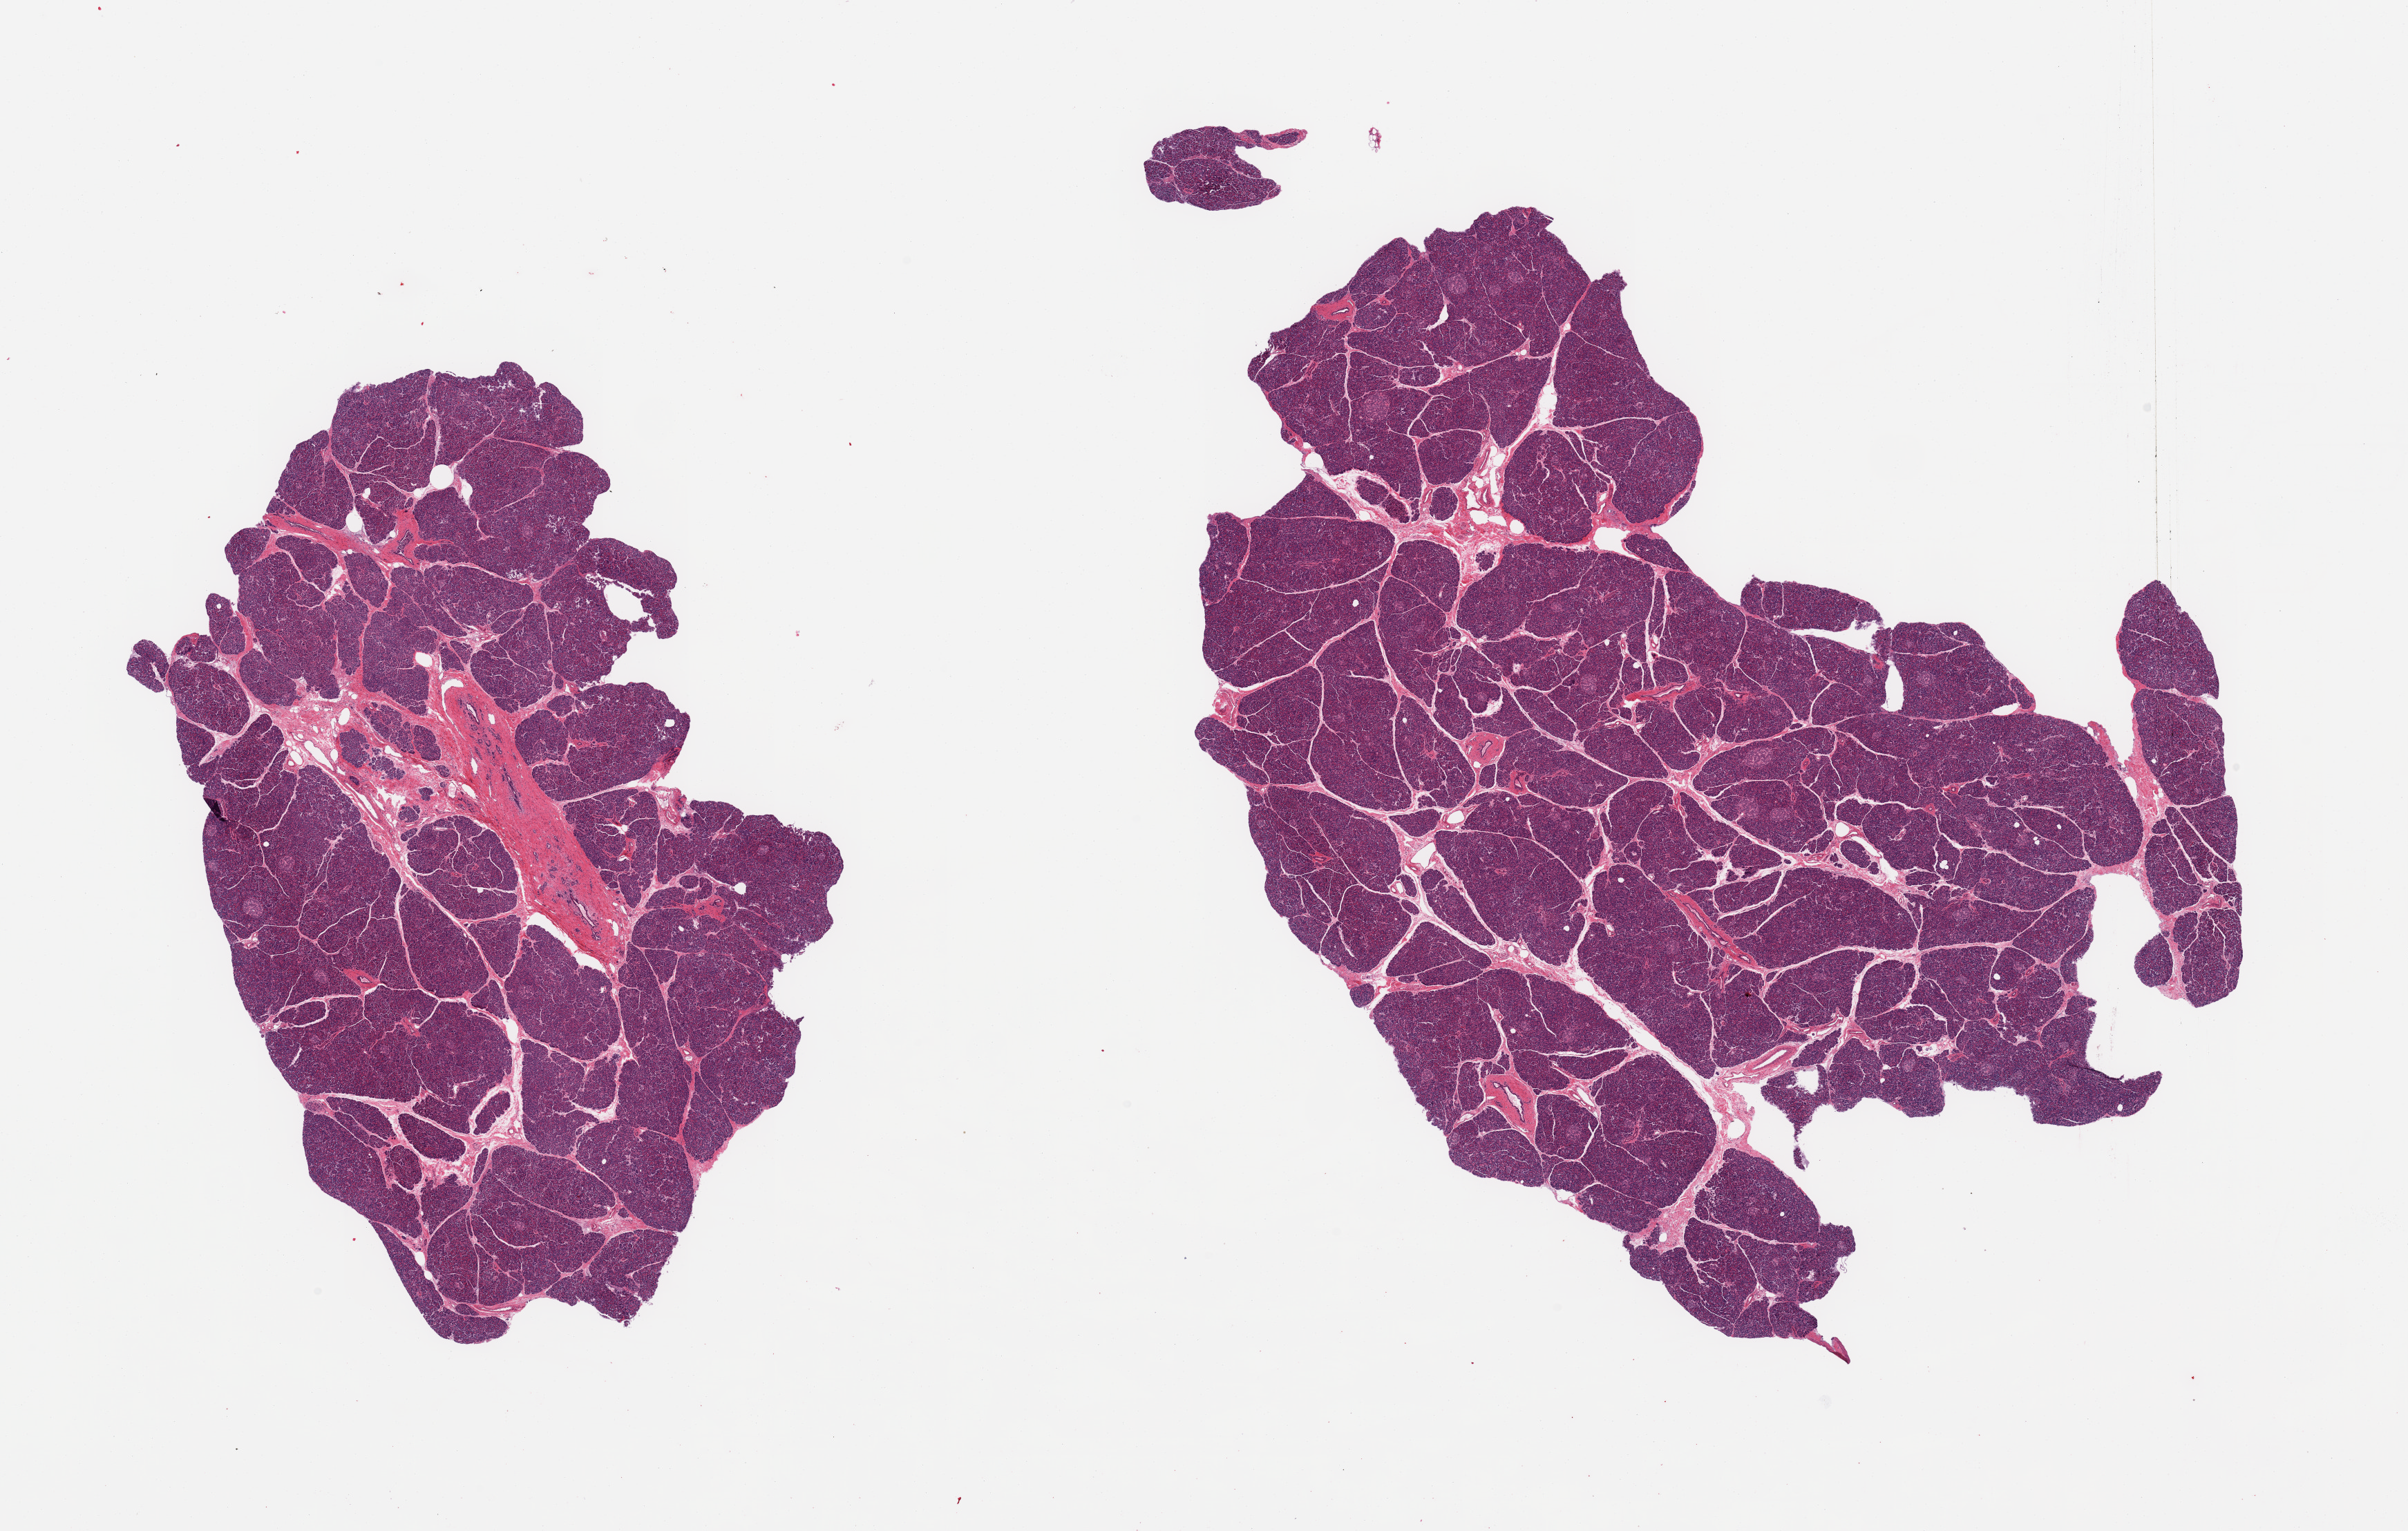
Whole-slide image, H&E stain — a low-resolution overview of the entire scanned area, about 27.6 x 17.5 mm. PAXgene-fixed, paraffin-embedded tissue. Section of pancreas (target tissue). Tissue donor sample. Donor sex: female.
Pathologist's review note for this sample: 2 pieces; plentiful islets.